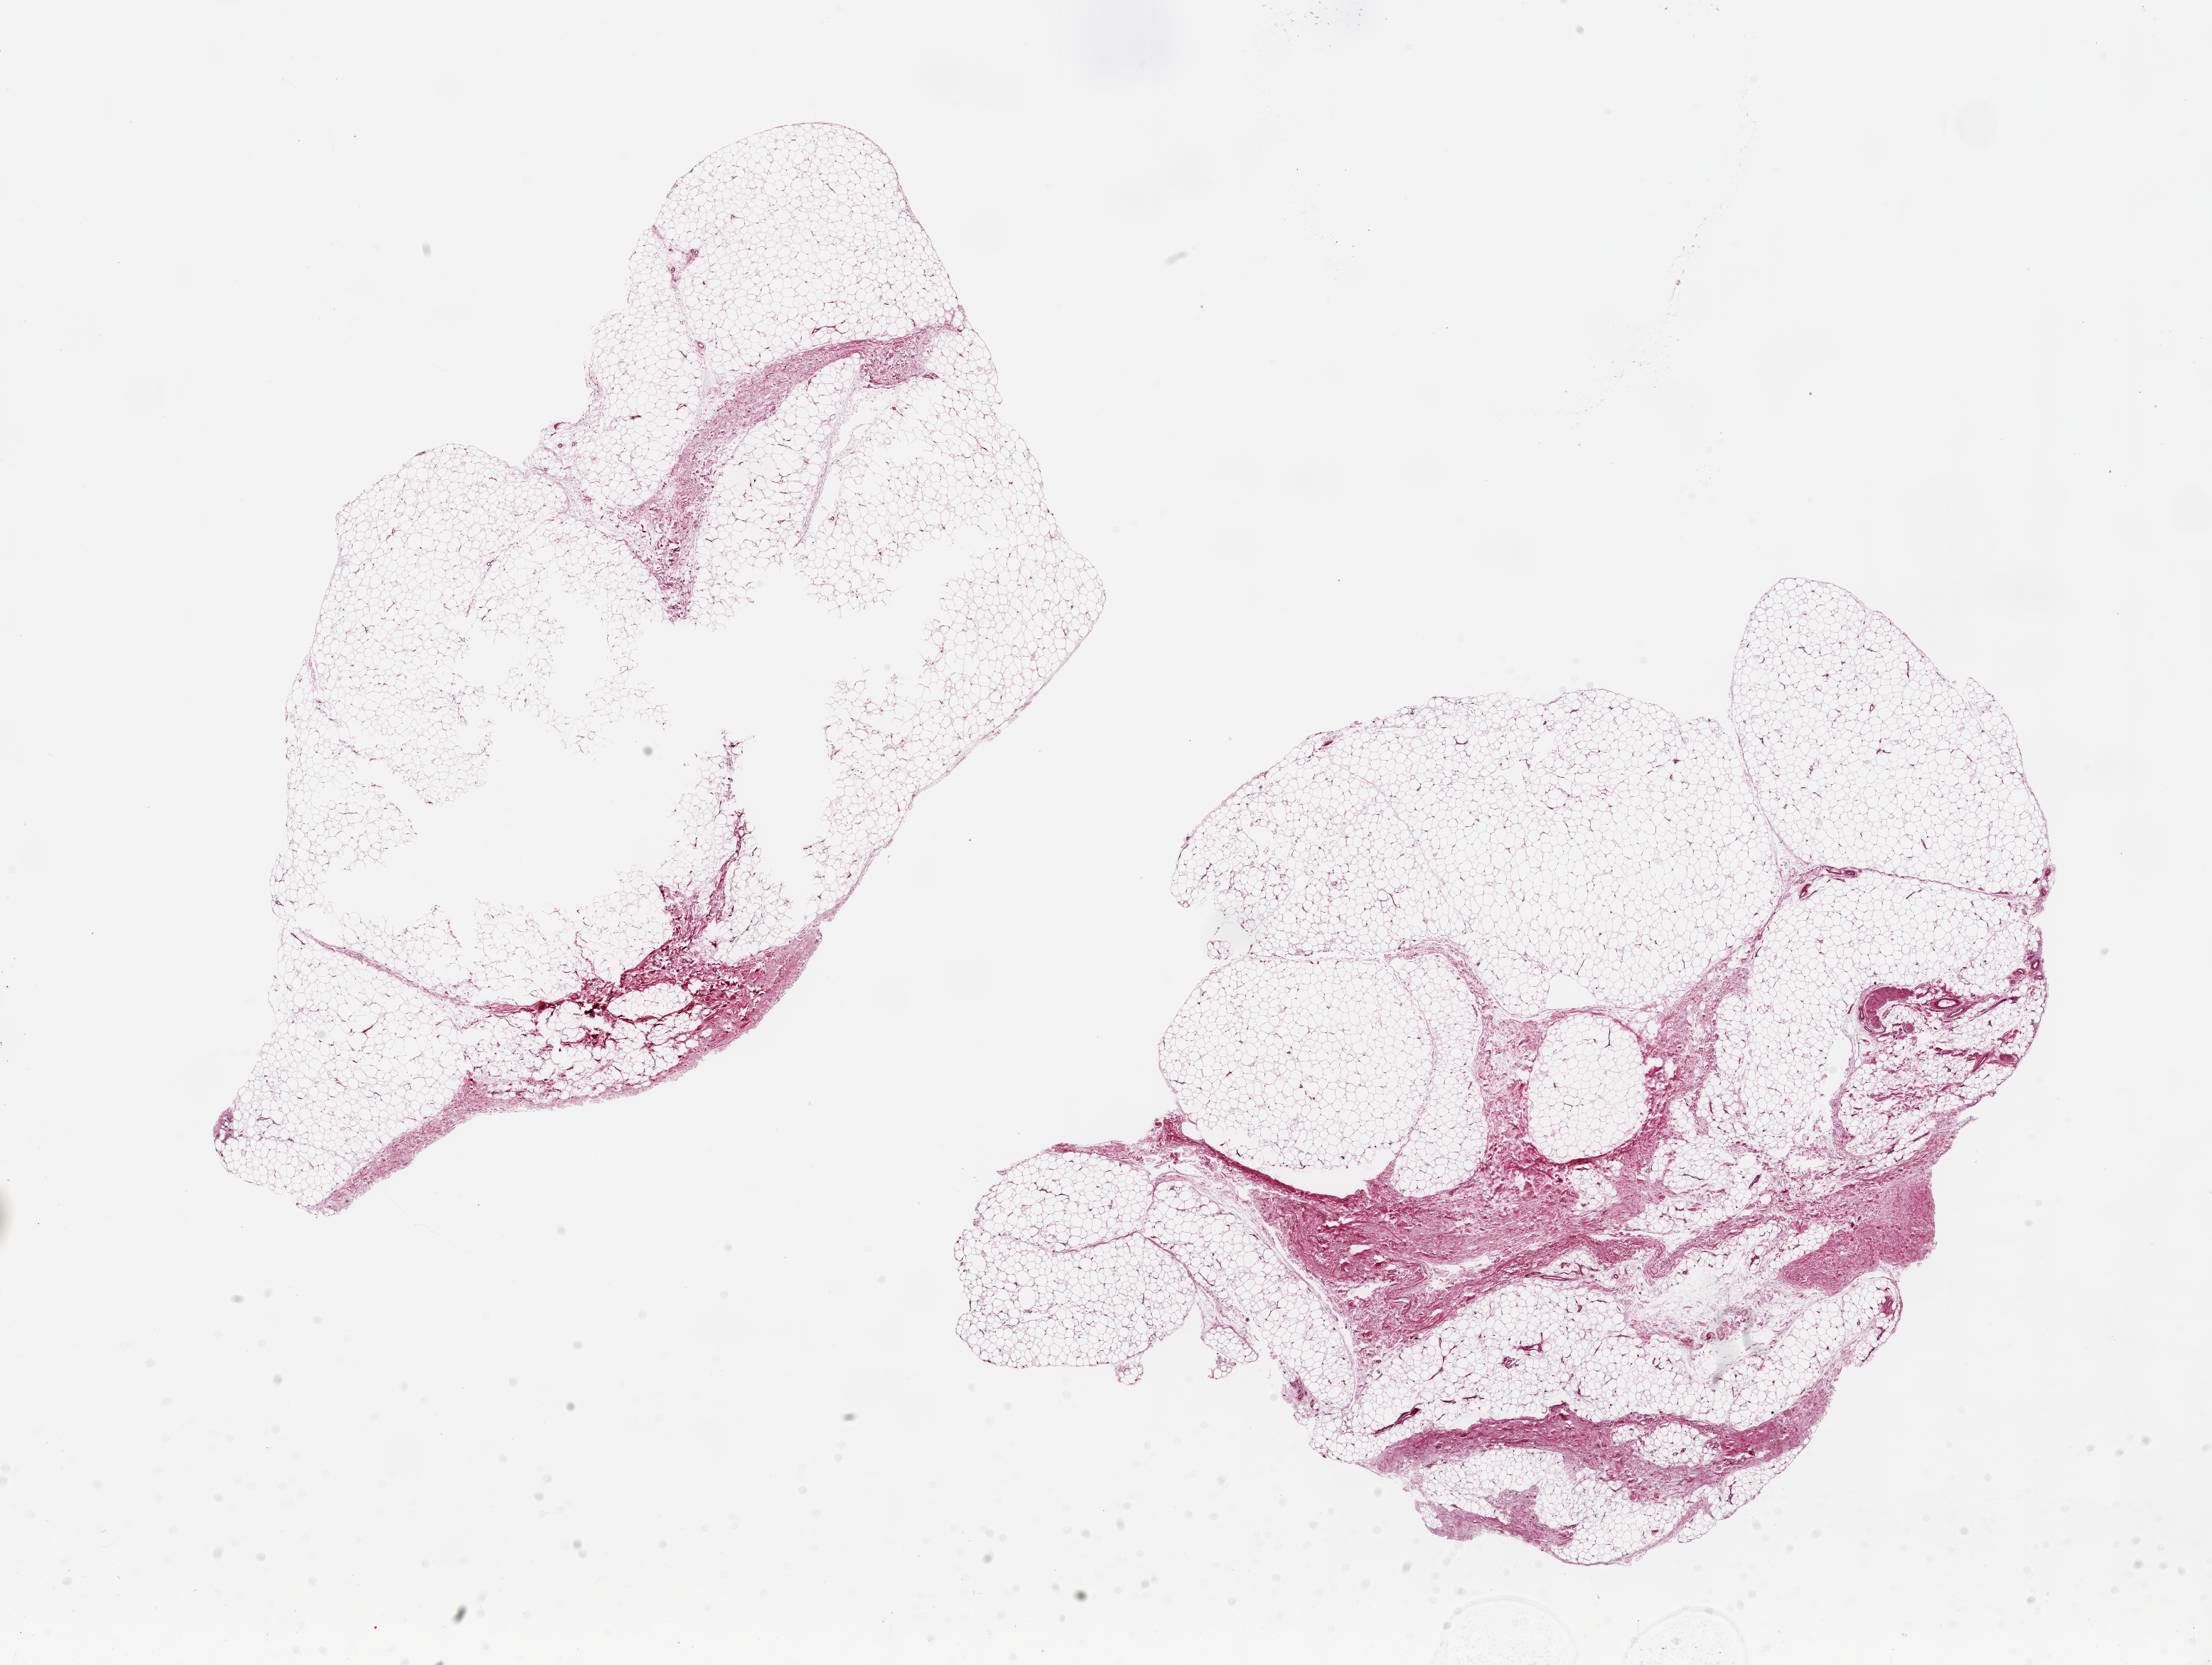
Whole-slide image, haematoxylin and eosin stain, brightfield, whole scanned area (about 24.6 x 18.5 mm) shown as a low-resolution overview; PAXgene-fixed paraffin-embedded (PFPE) section; target tissue: adipose tissue; donor tissue sample. Donor: male.
Pathologist's review note for this sample: 2 ~11x8m aliquots.